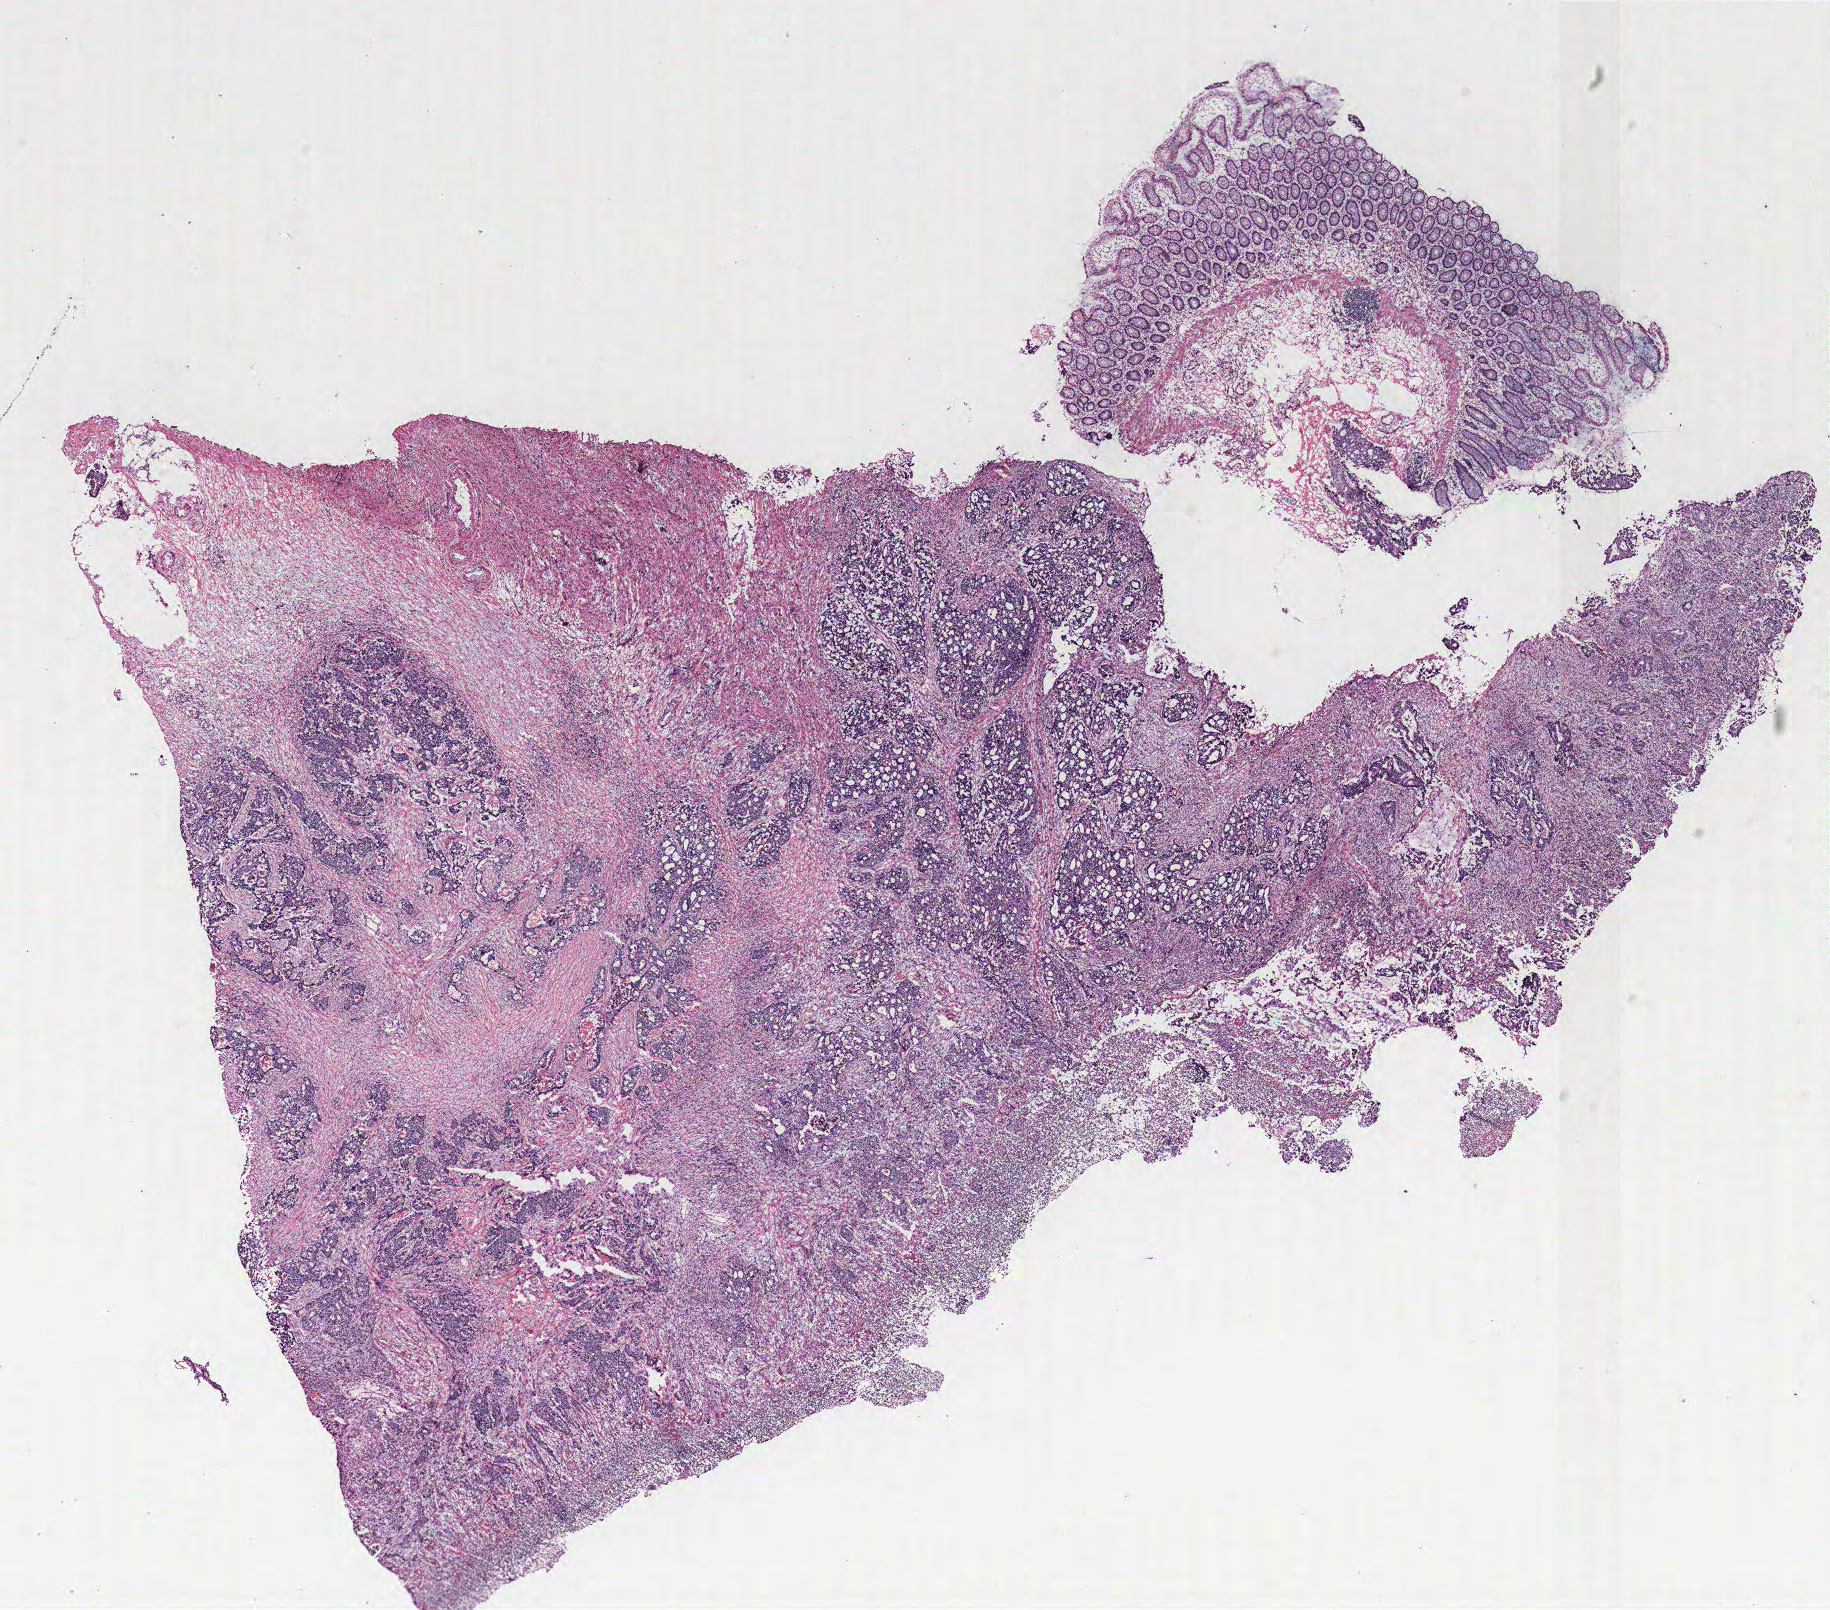
Whole-slide histology image, H&E — a low-resolution overview of the entire scanned area, about 14.6 x 12.9 mm (slide scanned at 40x); tumour tissue sample, colon. Male, 64 y/o.
Histologic diagnosis: Adenocarcinoma, NOS.